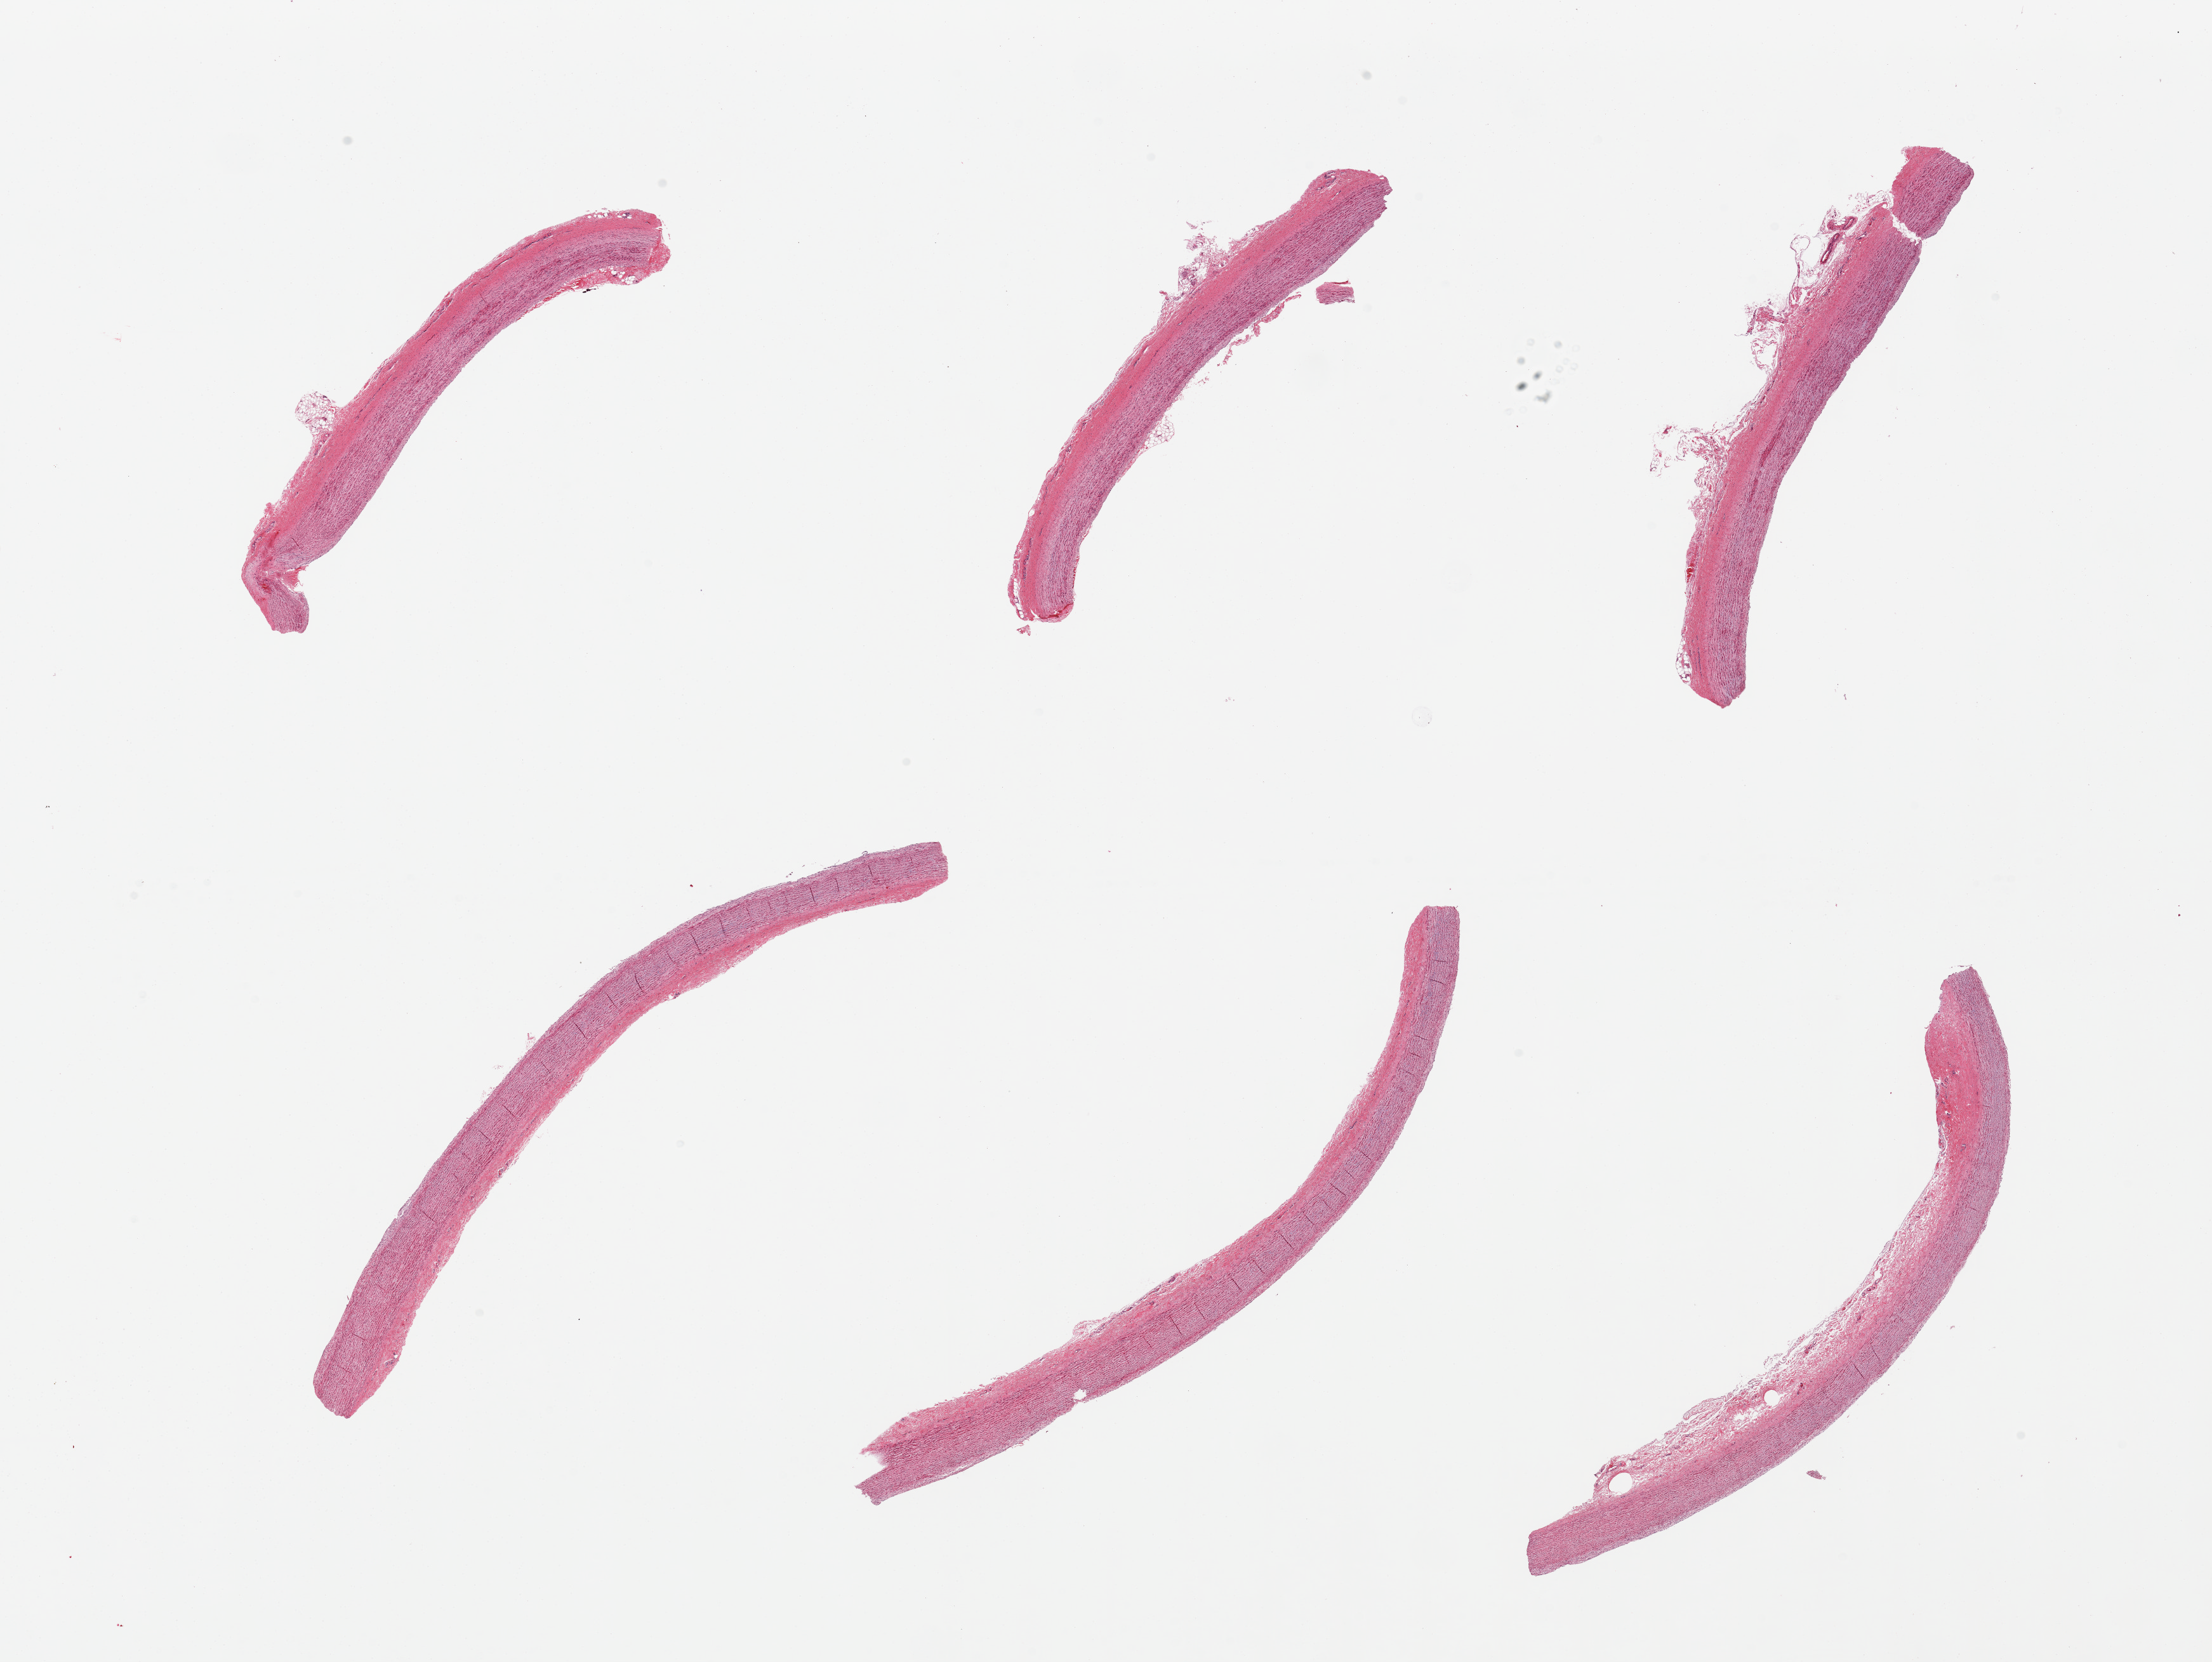
Digitized hematoxylin and eosin (H&E)-stained section, low-resolution overview of the scanned area, about 27.6 x 20.7 mm, PAXgene-fixed, paraffin-embedded tissue, sampled site (target tissue): aorta, donor tissue sample. Female donor.
Pathologist's review note for this sample: 6 pieces, minimal attached serosa.